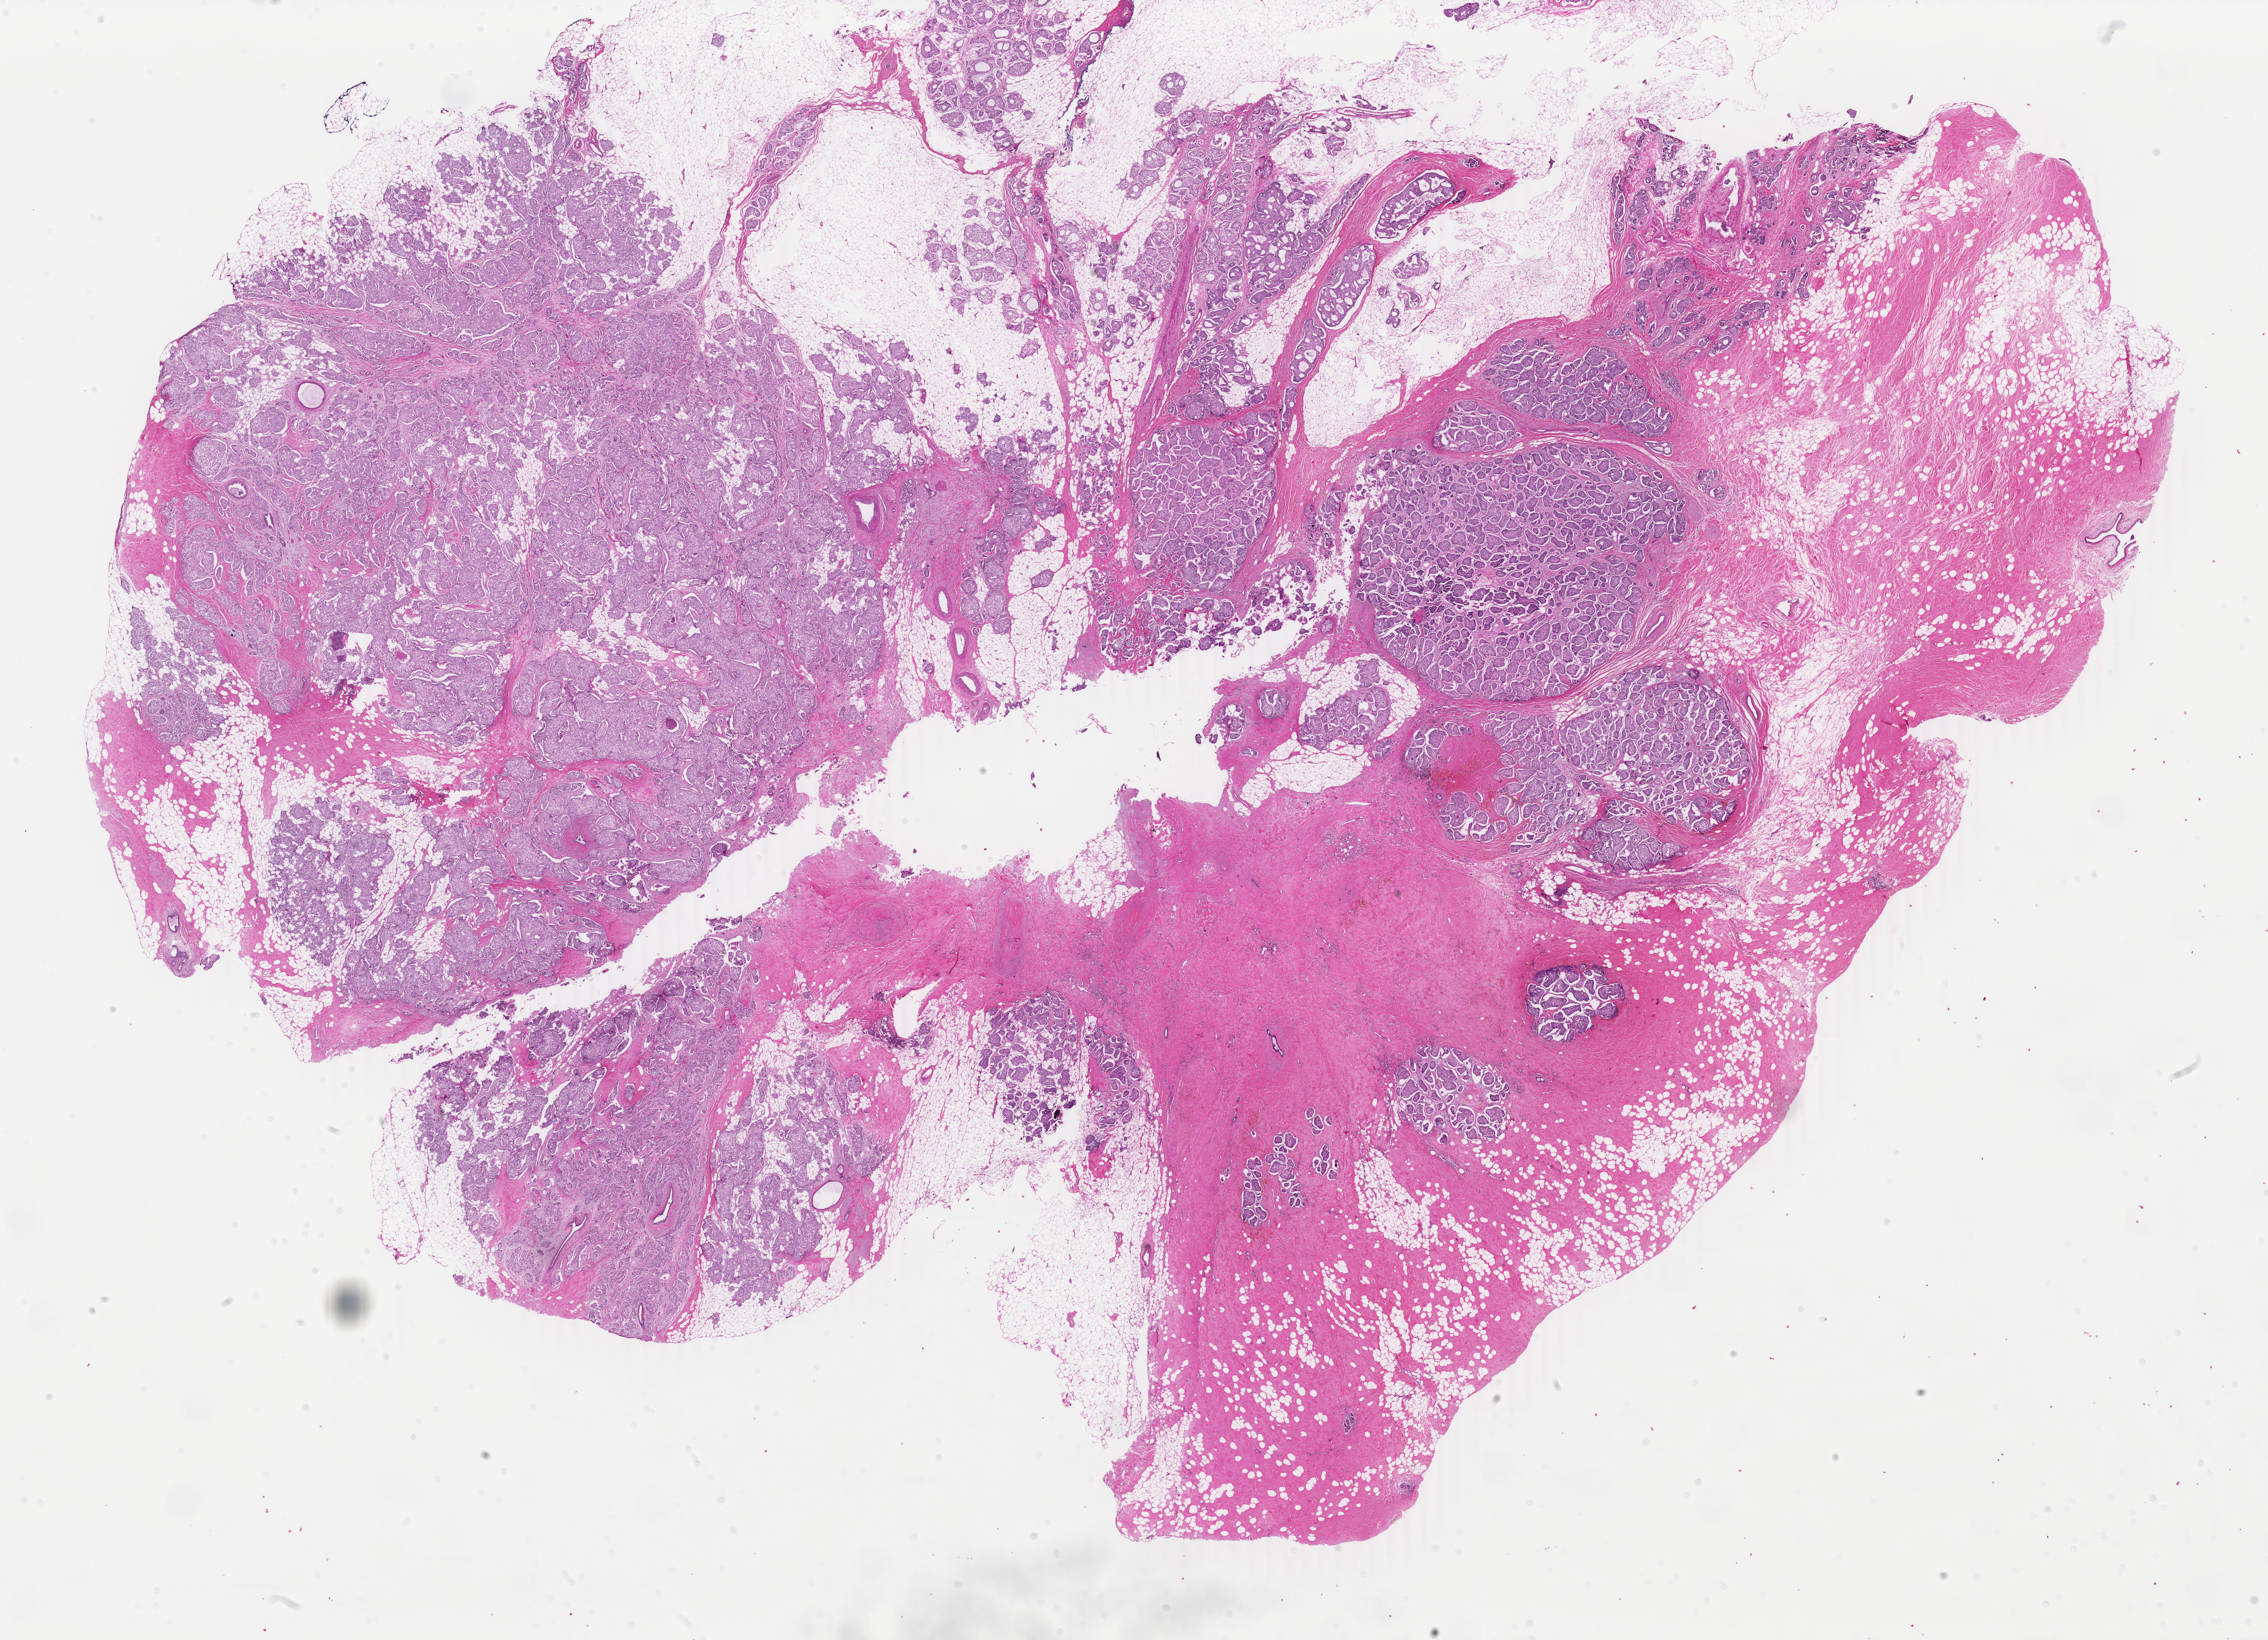
H&E whole-slide image — a low-resolution overview of the entire scanned area, about 31.2 x 22.5 mm; formalin-fixed paraffin-embedded (FFPE) diagnostic section; breast, primary tumour sample. Patient: female, age at initial diagnosis 73 years.
AJCC pathologic stage: IIA (6th edition). Diagnosis: Infiltrating duct carcinoma, NOS. Lymph nodes positive (case pathology): 0 of 1 examined.